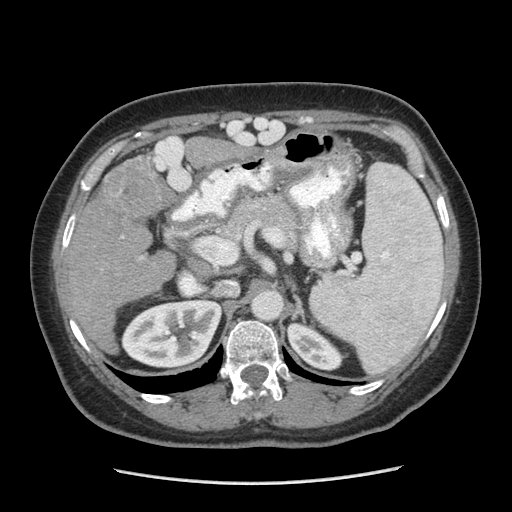
Contrast-enhanced abdominal CT (liver protocol), one axial slice; position 148 of 185 along the scan axis; reconstruction kernel STANDARD; 140 kVp; soft-tissue window (W 400 / L 40 HU); 2.5 mm slice thickness; 512 × 512 image matrix, field of view 360 × 360 mm. From the clinical record (not read from this slice): diagnosis: hepatocellular carcinoma (patient treated with transarterial chemoembolisation; whether this scan precedes or follows treatment is not stated here); TNM stage (as recorded): Stage-I; Child-Pugh class: A.
Outlined on this slice (semi-automatically segmented with operator editing):
- liver parenchyma outside the tumour (the mass and vessels are separate outlines, so this box may not span the whole liver): bounding box [x1, y1, x2, y2] px = [64, 136, 184, 342]
- mass: [101, 157, 170, 218]
- liver vessels: [68, 137, 184, 259]